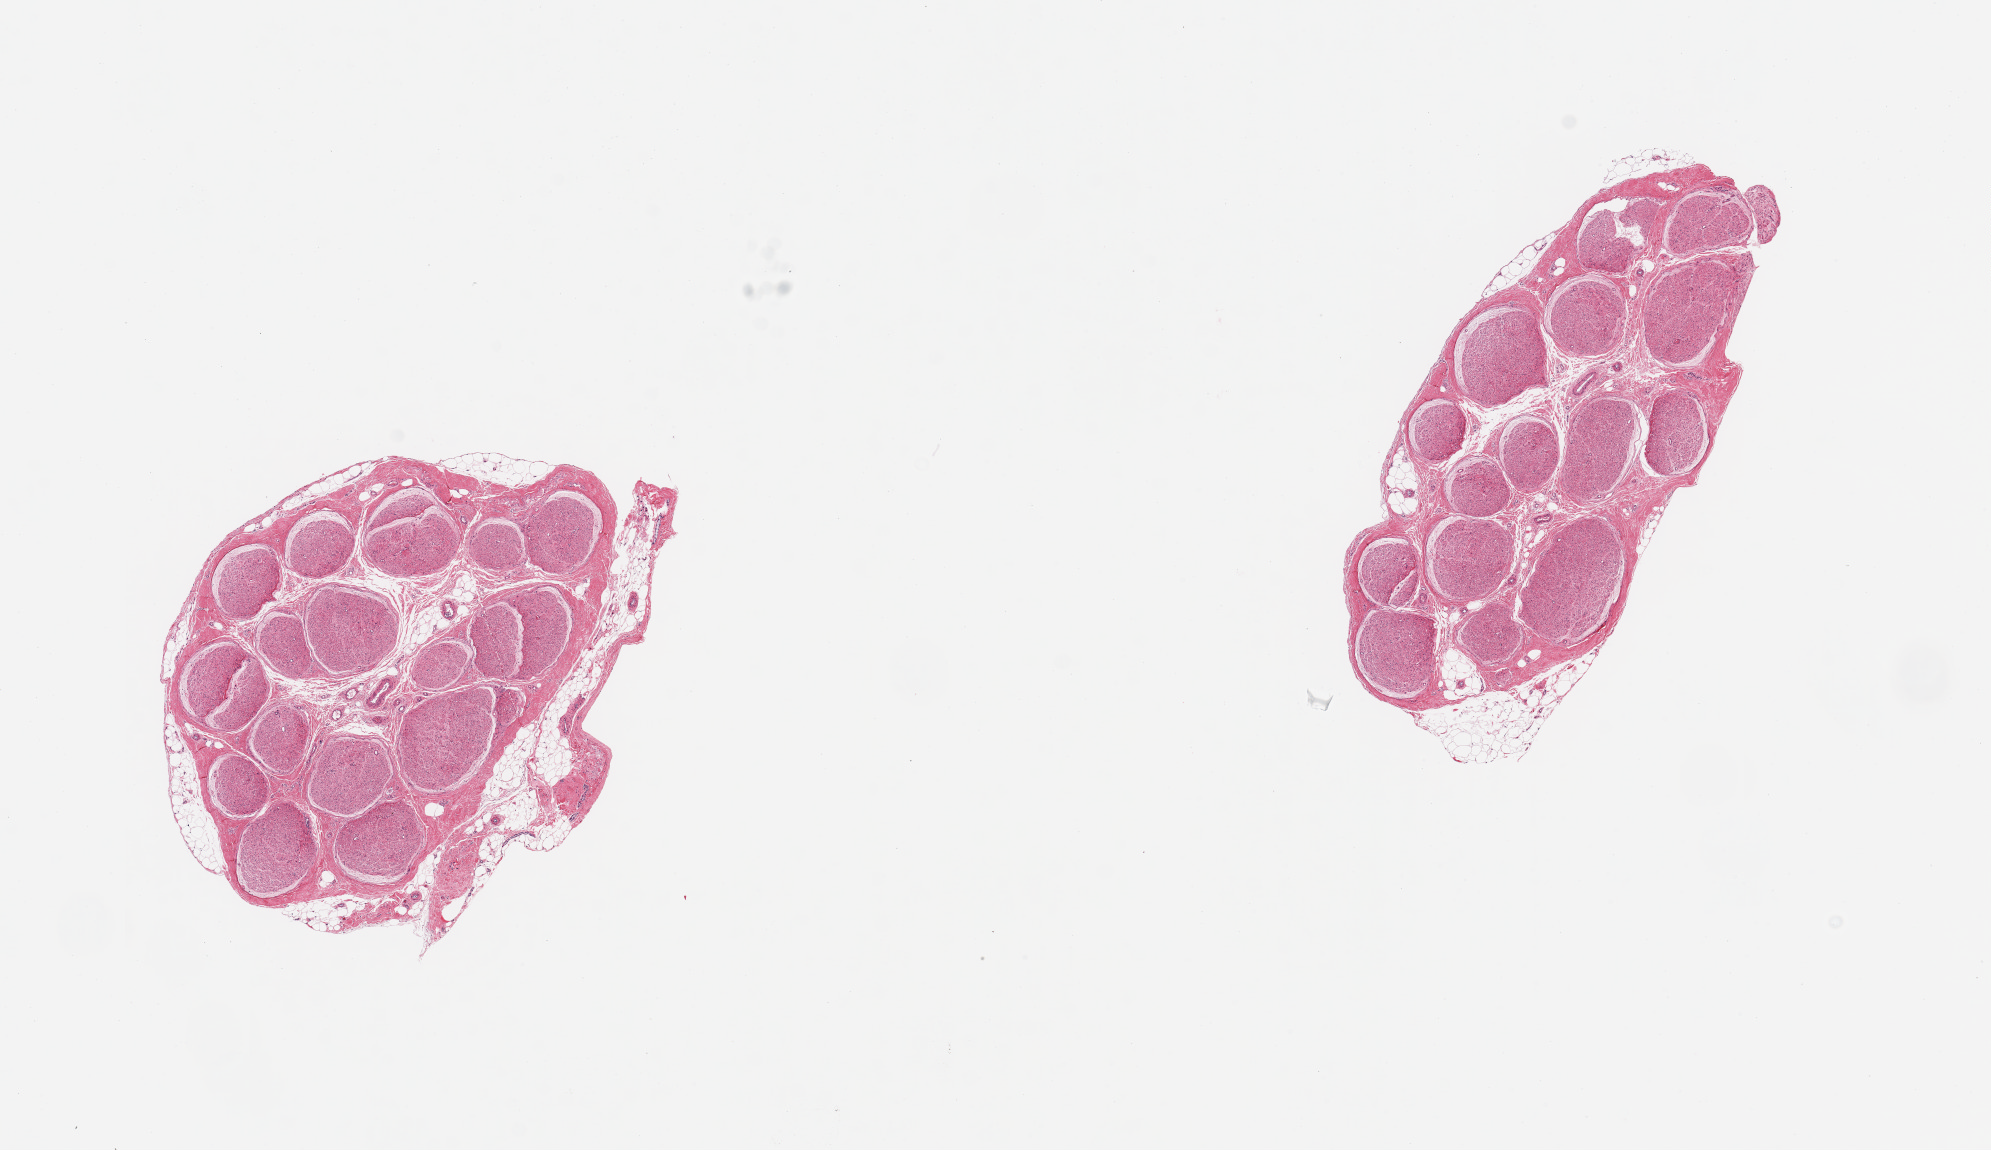
Digitized haematoxylin and eosin-stained section, brightfield — a low-resolution overview of the entire scanned area, about 15.8 x 9.1 mm. PAXgene-fixed paraffin-embedded (PFPE) section. Sampled site (target tissue): tibial nerve. Tissue donor sample. Donor sex: male.
- reviewer comment on this tissue sample: 2 pieces trace nubbin of fat up to ~0.5mm